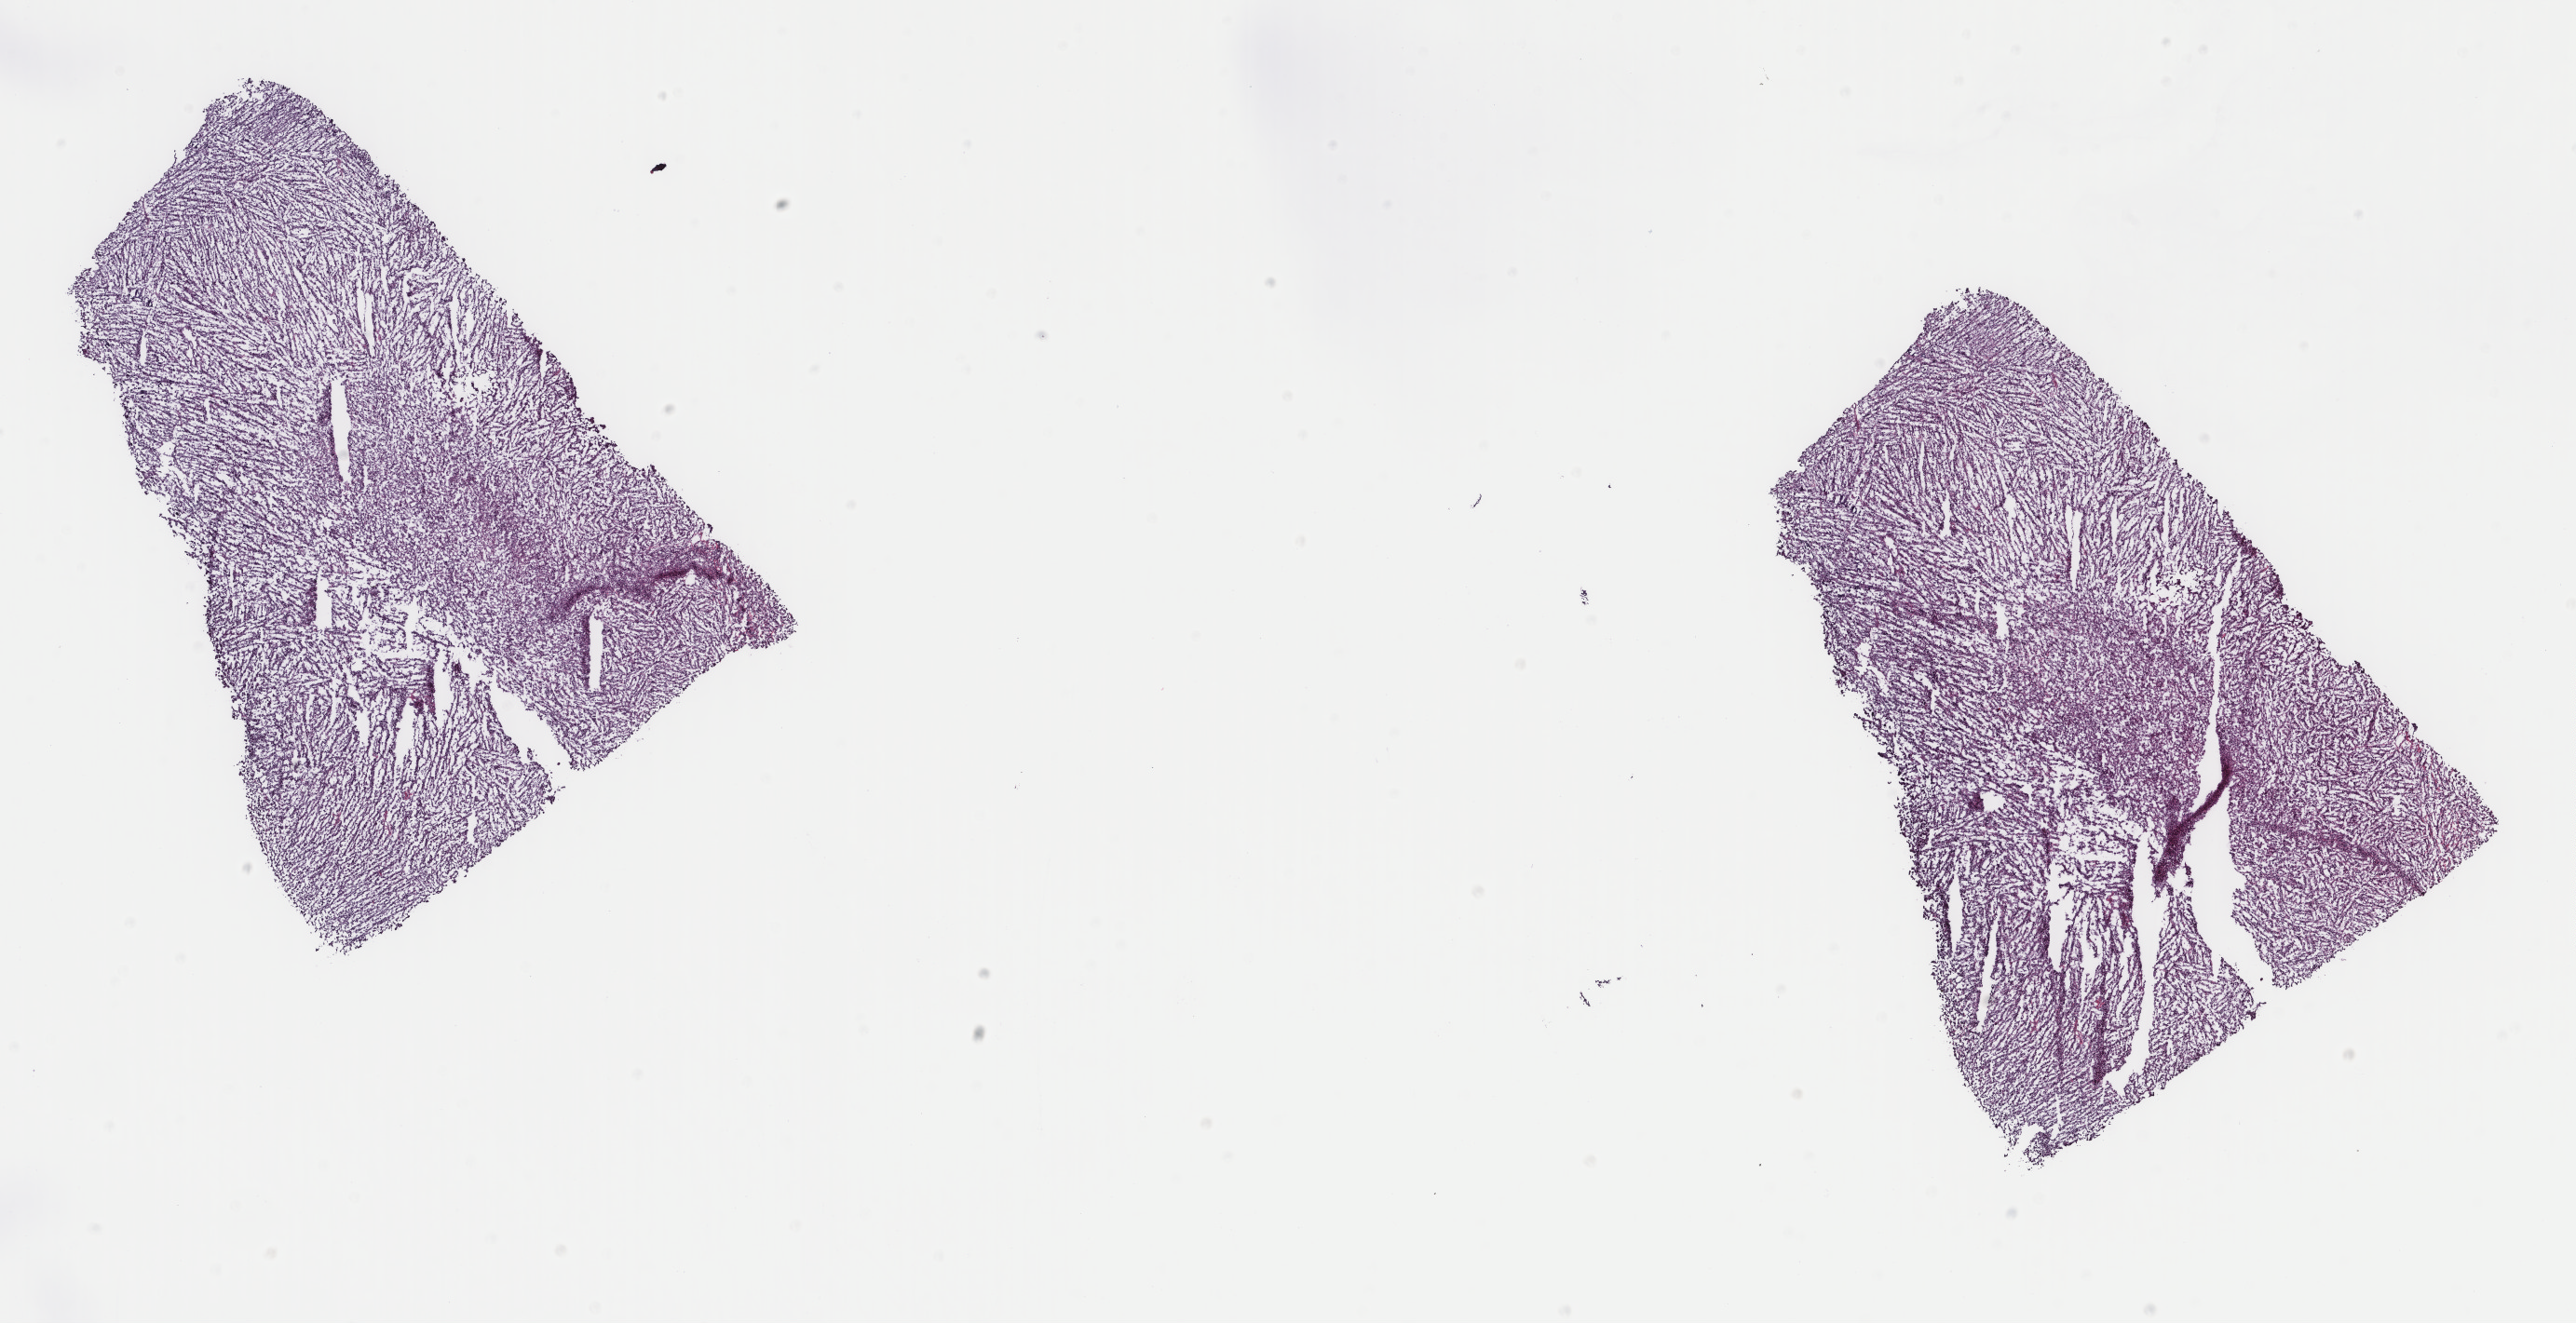
Whole-slide histology image, H&E-stained, whole scanned area (about 22.0 x 11.3 mm) shown as a low-resolution overview. Frozen section from the top of the tissue portion. Uterus, primary tumour sample. Female, age 55 years at initial diagnosis. Slide review estimates, as recorded: tumour cells 100%, tumour nuclei 95%, normal cells 0%, stromal cells 0%, necrosis 0%. Infiltration values recorded for this section: lymphocyte infiltration 0%, monocyte infiltration 0%, neutrophil infiltration 0%.
* pathologic diagnosis: Leiomyosarcoma, NOS